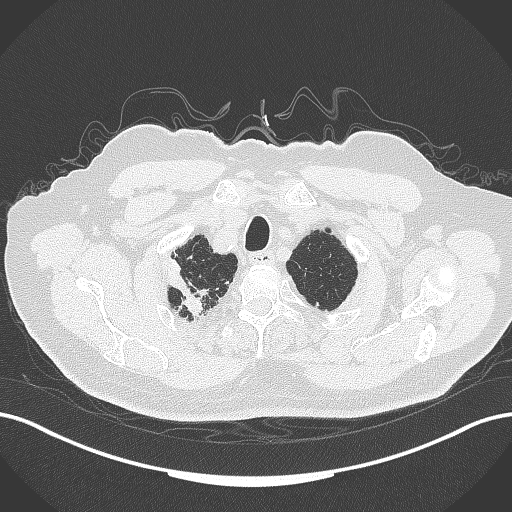
Chest CT, one axial slice. Slice 327 of 389 in the series (ordered by position). Reconstruction kernel B70f. 120 kVp. Lung window (W 1500 / L -600 HU). 512 × 512 image matrix, field of view 400 × 400 mm. Male patient, age 72 years. Case-level facts recorded for this patient, not image findings: clinical TNM (as recorded): T1a N0 M0.
Annotated regions visible in this slice (bounding box drawn by a radiologist):
- lung tumour (recorded histology: squamous cell carcinoma): bounding box (x1, y1, x2, y2) in pixels: (158, 252, 202, 320)